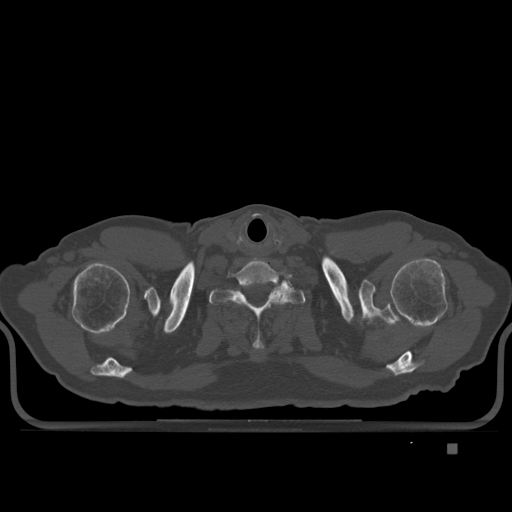
CT including the spine, one axial slice. Position 329 of 435 along the scan axis. Bone window (W 1800 / L 400 HU). 512 × 512 image matrix, field of view 434 × 434 mm. Patient: male, 73 years. From the clinical record (not read from this slice): primary cancer: skin.
Structures marked on this image (semi-automatic segmentation, software-assisted and operator-edited):
- T1 vertebra: bounding box [x1, y1, x2, y2] px = [210, 282, 305, 351]